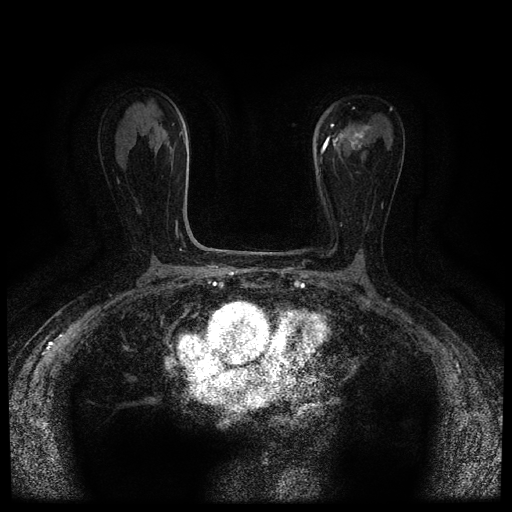
Breast MRI (dynamic contrast-enhanced, multi-phase), one axial slice; position 46 of 116 along the scan axis; dynamic contrast-enhanced series, time point 2 of 5 at this slice position (early post-contrast); 1.5 T; TE 2.7 ms, TR 5.4 ms; 512 × 512 image matrix, field of view 320 × 320 mm. Female patient, age 80 years.
Outlined on this slice (semi-automatically segmented with operator editing):
- breast lesion (labelled 'tumour' in the annotation; benign lesions carry a separate 'benign' label): bounding box [x1, y1, x2, y2] px = [332, 125, 369, 149]